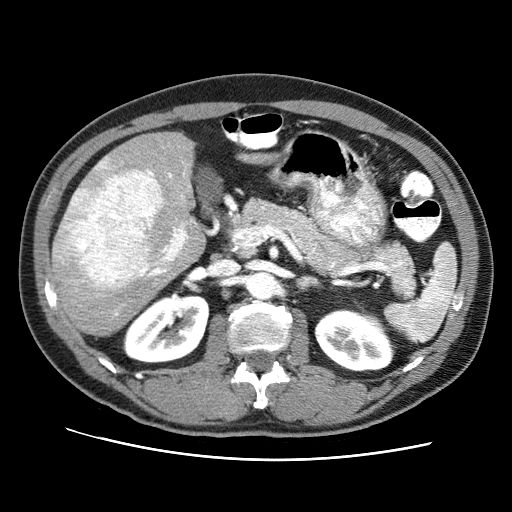
Contrast-enhanced abdominal CT (liver protocol), one axial slice. Slice 39 of 71 in the series (ordered by position). Reconstruction kernel STANDARD. 120 kVp. Soft-tissue window (W 400 / L 40 HU). 2.5 mm slice thickness. 512 × 512 image matrix, field of view 360 × 360 mm. Case-level facts recorded for this patient, not image findings: diagnosis: hepatocellular carcinoma (patient treated with transarterial chemoembolisation; whether this scan precedes or follows treatment is not stated here); TNM stage (as recorded): Stage-II; Child-Pugh class: A; tumour differentiation: well differentiated; tumour nodularity: multinodular.
Structures marked on this image (semi-automatically segmented with operator editing):
- liver parenchyma outside the tumour (the mass and vessels are separate outlines, so this box may not span the whole liver): bounding box (x1, y1, x2, y2) in pixels: (52, 132, 277, 336)
- mass: (53, 169, 162, 292)
- liver vessels: (65, 158, 188, 315)